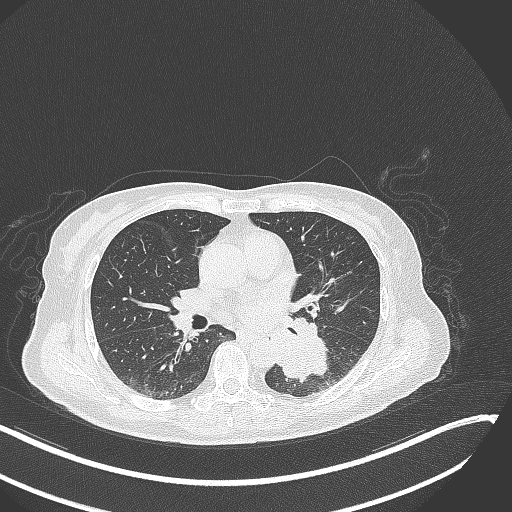
Chest CT, one axial slice; slice 142 of 342 in the series (ordered by position); 120 kVp; lung window (W 1500 / L -600 HU); 1 mm slice thickness; 512 × 512 image matrix, field of view 400 × 400 mm. Female patient, age 64 years. Case-level facts recorded for this patient, not image findings: clinical TNM (as recorded): T3 N1 M1.
Structures marked on this image (bounding box drawn by a radiologist):
- lung tumour (recorded histology: small cell carcinoma): bounding box [x1, y1, x2, y2] px = [269, 325, 334, 386]